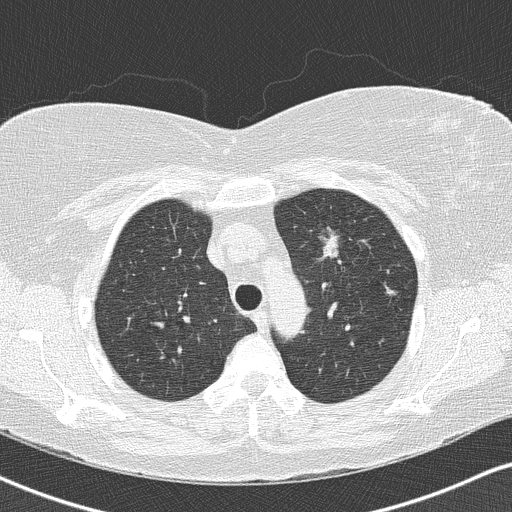
Low-dose screening chest CT, axial slice, second screening round (one year after baseline), lung window (W 1500 / L -600 HU), 120 kVp, 512 × 512 image matrix, field of view 328 × 328 mm. Female, age 57 years at enrolment. Current smoker at enrolment.
Expert reader's lesion annotation, bounding box <312,223,349,265> (left, top, right, bottom; pixels). The screening reader recorded 3 non-calcified nodules or masses ≥4 mm on this exam (left upper lobe, right upper lobe, right middle lobe); which of them this box marks is not recorded.